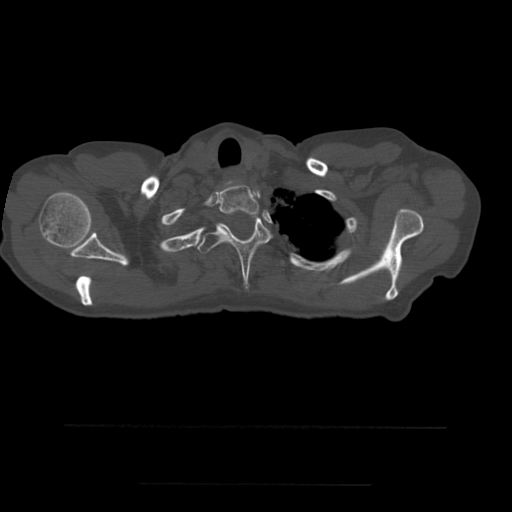
CT including the spine, one axial slice. Position 438 of 544 along the scan axis. Bone window (W 1800 / L 400 HU). 512 × 512 image matrix, field of view 350 × 350 mm. Patient age 58 years. Case-level facts recorded for this patient, not image findings: primary cancer: lung.
Structures marked on this image (semi-automatic segmentation, software-assisted and operator-edited):
- T1 vertebra: bounding box [x1, y1, x2, y2] px = [219, 184, 259, 216]
- T2 vertebra: [198, 215, 272, 288]